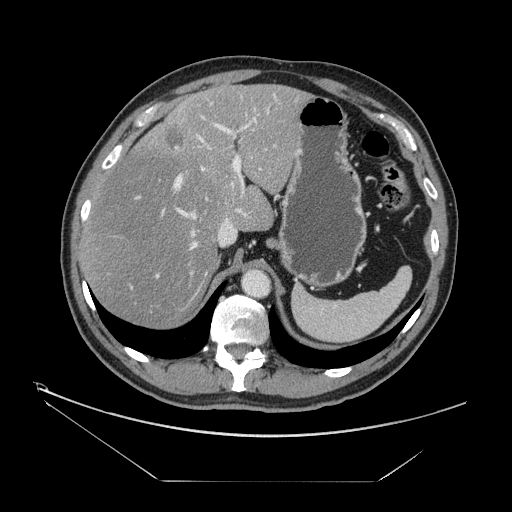
Contrast-enhanced abdominal CT, one axial slice. Position 108 of 161 along the scan axis. 120 kVp. Intravenous contrast given. Soft-tissue window (W 400 / L 40 HU). 2.5 mm slice thickness. 512 × 512 image matrix, field of view 440 × 440 mm. Male patient, age 65 years. Case-level facts recorded for this patient, not image findings: diagnosis: colorectal cancer liver metastases, imaged before liver resection; multiple liver metastases: yes; largest metastasis: 4.2 cm; disease in both lobes: yes.
Outlined on this slice (manually delineated by an expert):
- hepatic veins: bounding box (x1, y1, x2, y2) in pixels: (178, 135, 234, 250)
- liver: (83, 84, 306, 329)
- planned liver remnant (the part of the liver to remain after resection): (83, 85, 305, 329)
- portal vein (with intrahepatic branches): (135, 93, 278, 277)
- liver metastasis: (166, 130, 186, 149)